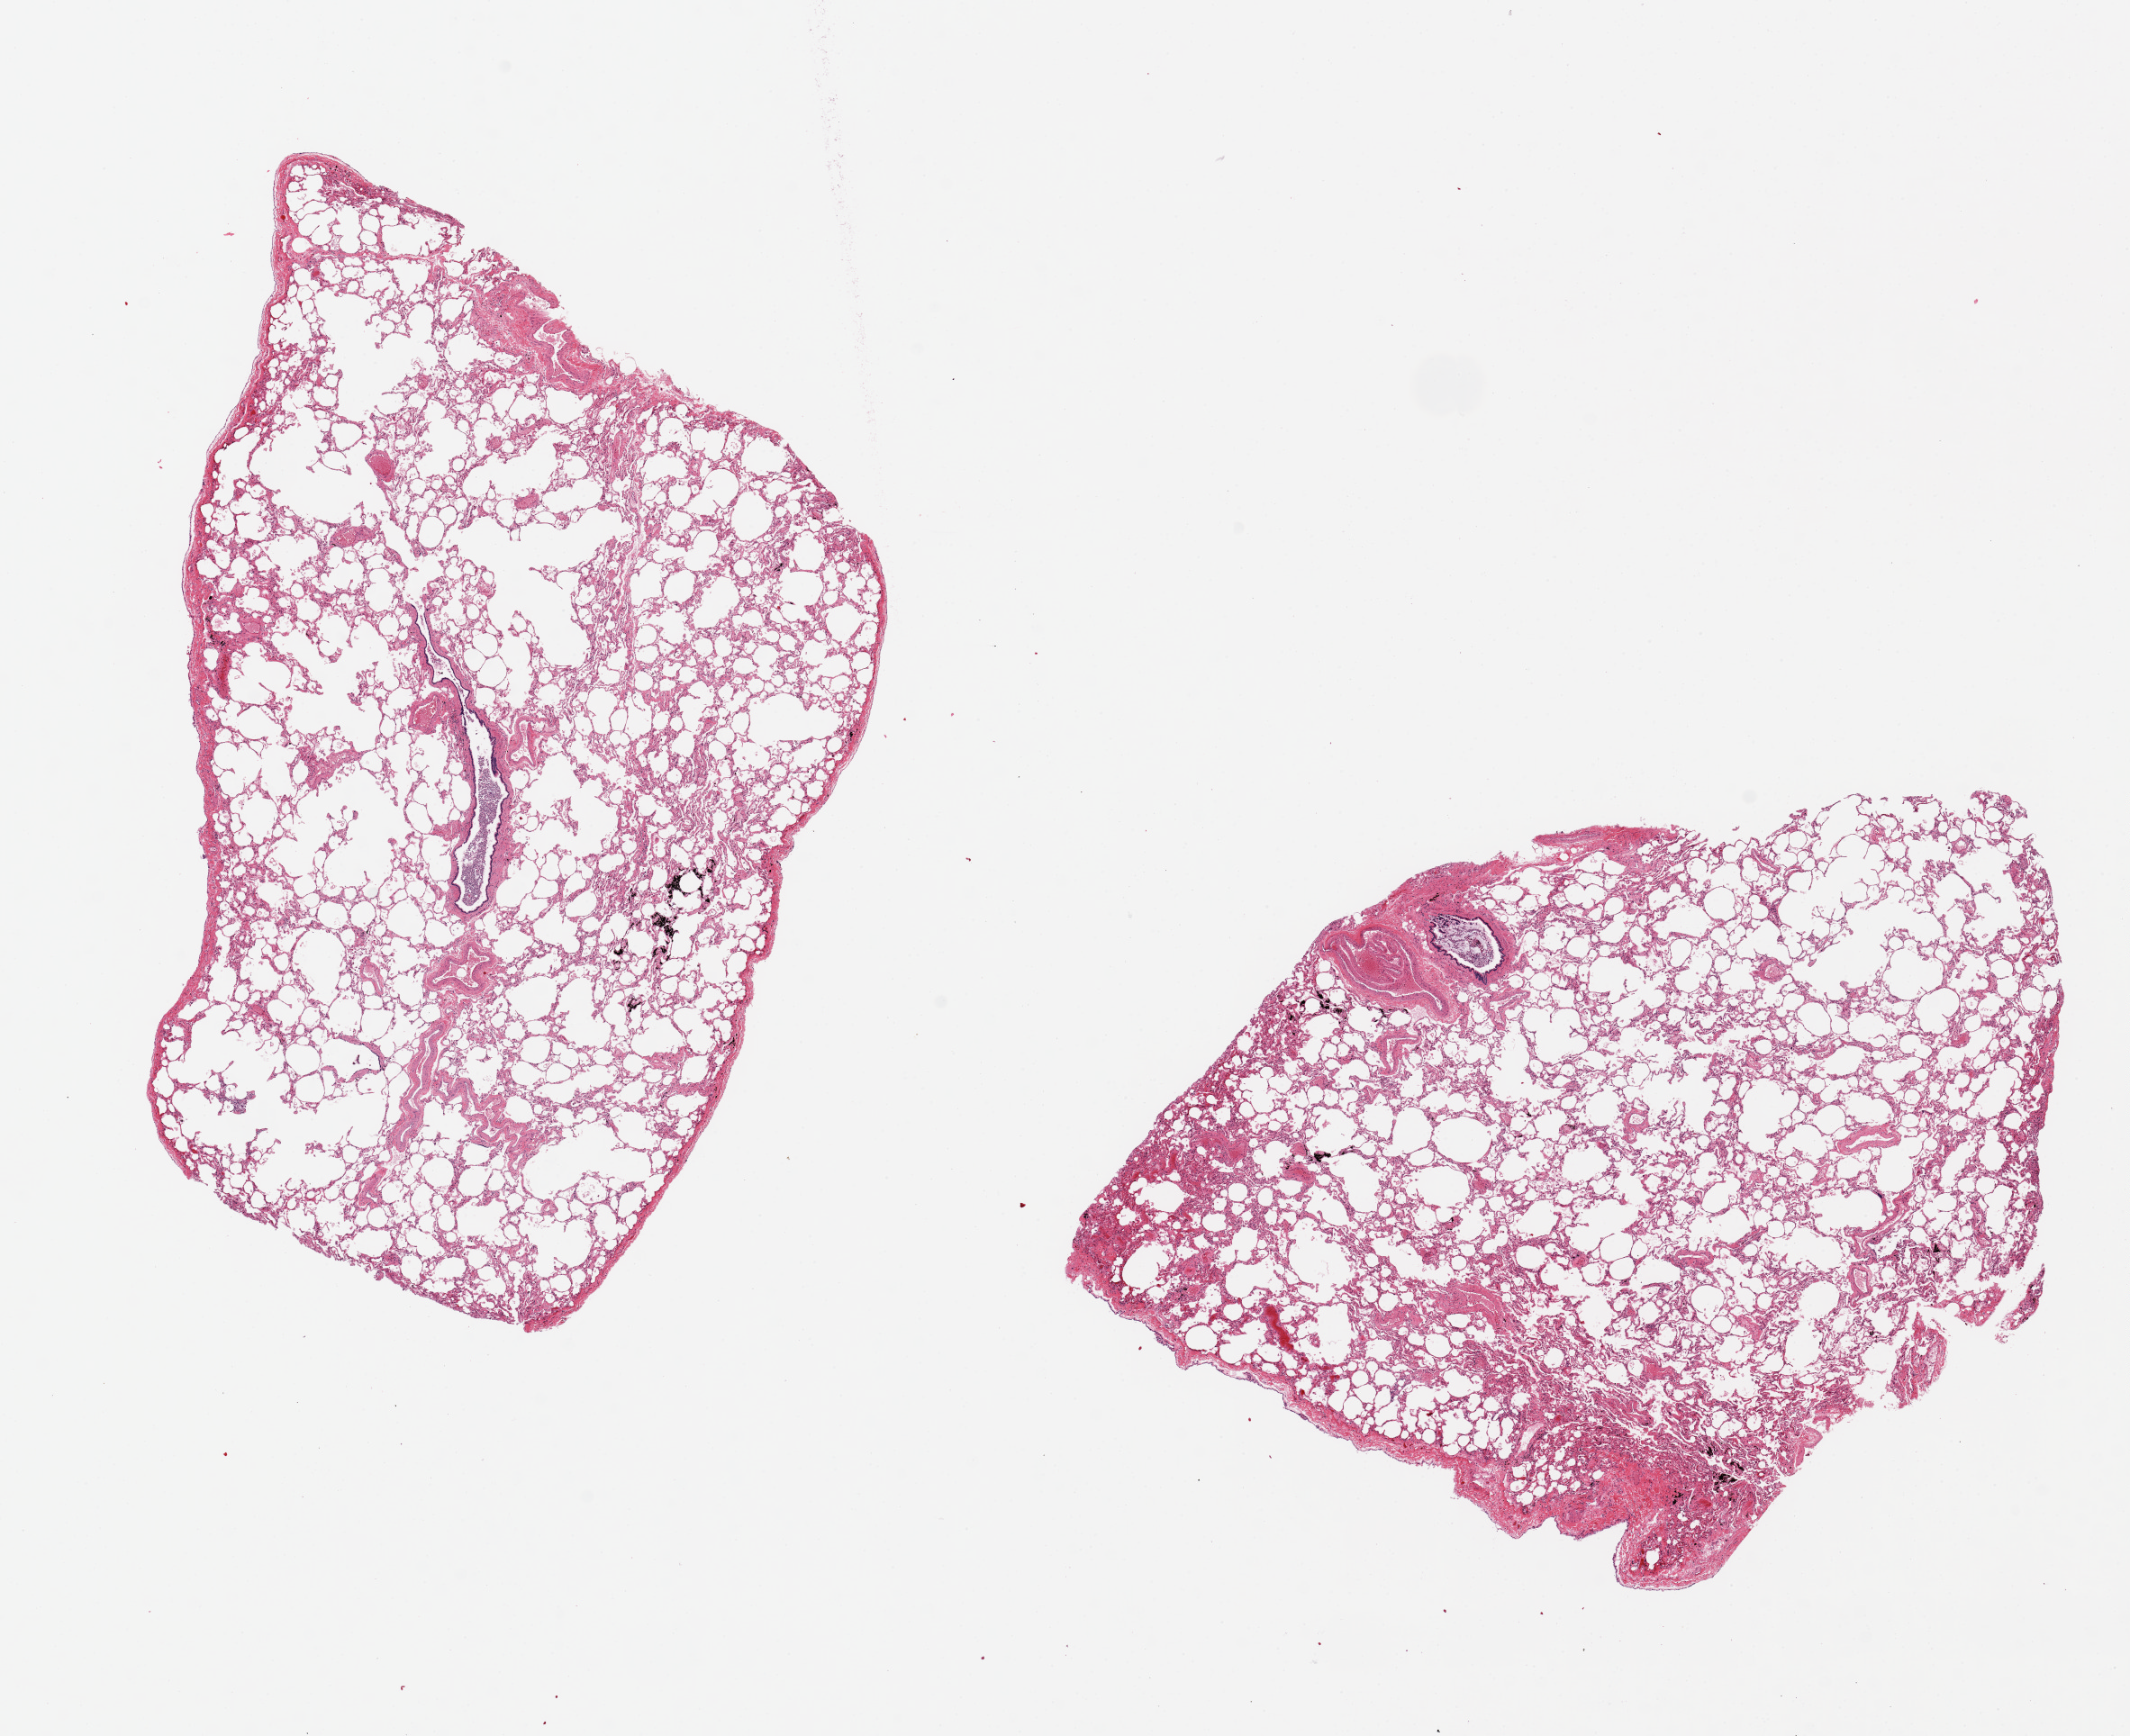
Whole-slide image, H&E stain, a low-resolution overview of the entire scanned area, about 18.7 x 15.2 mm (slide scanned at 20x), PAXgene-fixed, paraffin-embedded tissue, section of lung (target tissue), tissue donor sample. Donor: male.
Review note (as recorded): 2 pieces, 9x7 & 8x7mm; Mucopurulent exudates in bronchi, but no pneumonia.